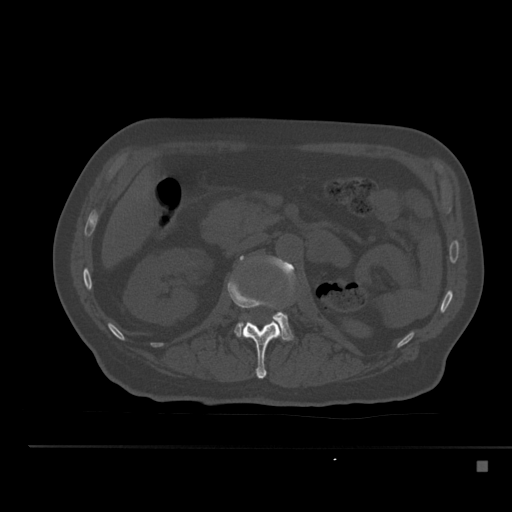
CT including the spine, one axial slice. Slice 200 of 517 in the series (ordered by position). Reconstruction kernel Br40s. 120 kVp. Bone window (W 1800 / L 400 HU). 1.5 mm slice thickness. 512 × 512 image matrix. Male patient, age 70 years. From the clinical record (not read from this slice): primary cancer: renal; vertebrae with lytic lesions (as recorded): T4, T6, T10, T12, L3, L4, L5.
Annotated regions visible in this slice (semi-automatic segmentation, software-assisted and operator-edited):
- L1 vertebra: box from (x=228, y=276) to (x=281, y=379) px
- L2 vertebra: (x=234, y=256)–(x=294, y=340)